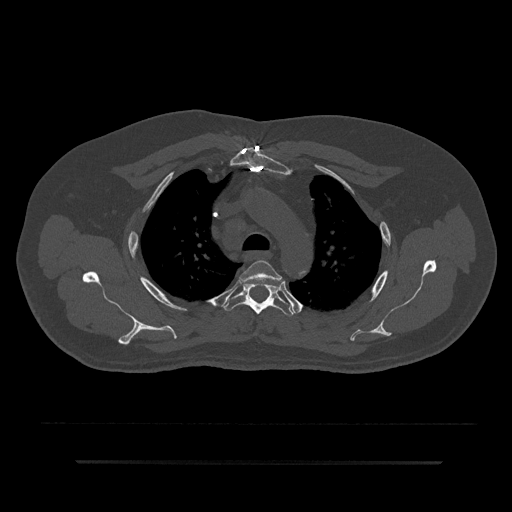
CT including the spine, one axial slice. Slice 631 of 797 in the series (ordered by position). 120 kVp. Bone window (W 1800 / L 400 HU). 0.5 mm slice thickness. 512 × 512 image matrix. Male patient, age 59 years. Case-level facts recorded for this patient, not image findings: primary cancer: bile ducts.
Annotated regions visible in this slice (semi-automatic segmentation, software-assisted and operator-edited):
- T3 vertebra: bounding box [x1, y1, x2, y2] px = [239, 260, 283, 284]
- T4 vertebra: [222, 282, 294, 316]